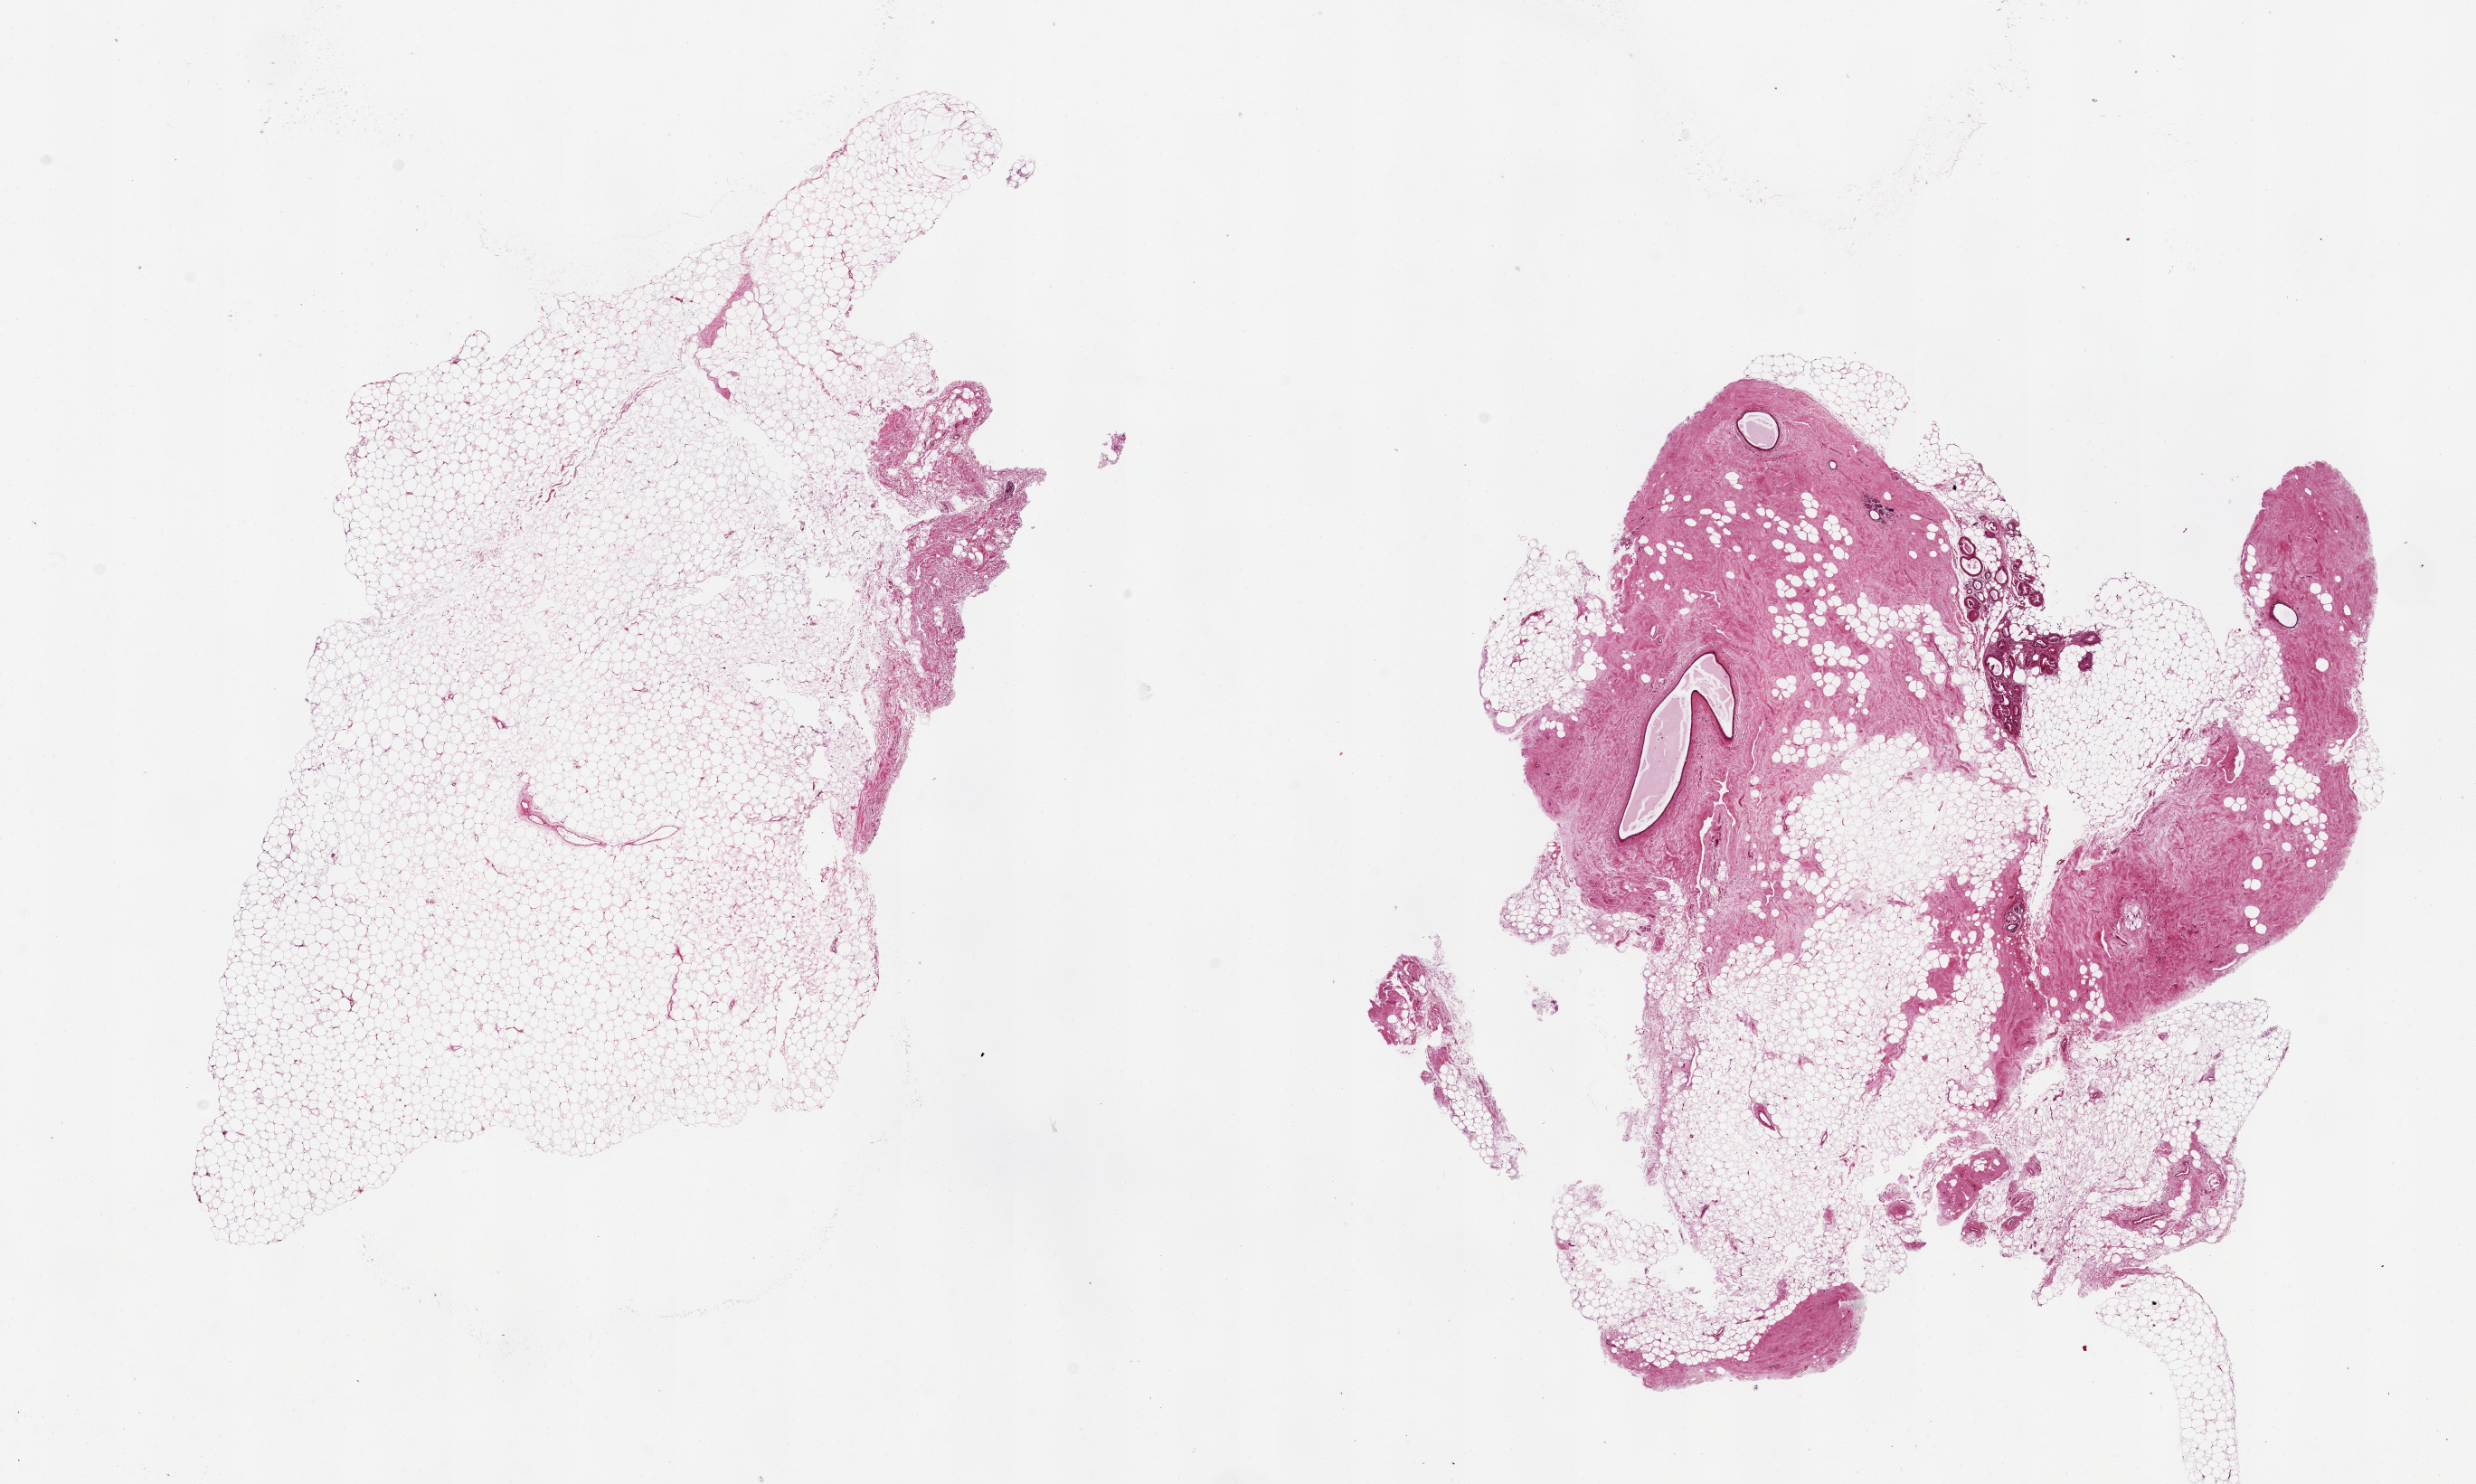
Whole-slide image, hematoxylin and eosin (H&E) stain, shown as a low-resolution overview of the whole scanned area (about 21.7 x 13.0 mm, from a 20x scan); PAXgene-fixed, paraffin-embedded tissue; target tissue: breast; donor tissue sample. Female donor.
Review note (as recorded): 2 pieces, 12x6.5 & 9x9mm. Ducts and lobules with apocrine change in 1 piece. Fibrocystic change. 90% adipose in other piece.